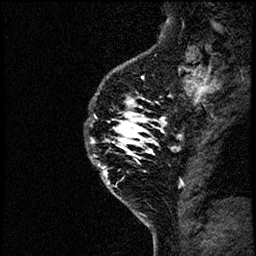
Breast MRI (dynamic contrast-enhanced), one sagittal slice; position 51 of 60 along the scan axis; dynamic contrast-enhanced study with each time point stored as its own series, time point 2 of 4 at this slice position (early post-contrast, ordered by acquisition time); 1.5 T; TE 4.2 ms, TR 17.6 ms; 2 mm slice thickness; 256 × 256 image matrix, field of view 200 × 200 mm. Female patient, age 40 years. From the clinical record (not read from this slice): setting: breast cancer imaged before/during neoadjuvant chemotherapy; receptor status: HER2-positive.
Annotated regions visible in this slice (semi-automatically segmented with operator editing):
- analysis volume of interest (the breast-tissue region the enhancement analysis was run in; not a lesion): box from (x=79, y=55) to (x=185, y=206) px
- tumour enhancement mask (voxels above the 100 % enhancement threshold inside the analysis volume of interest): (x=89, y=81)–(x=185, y=187)